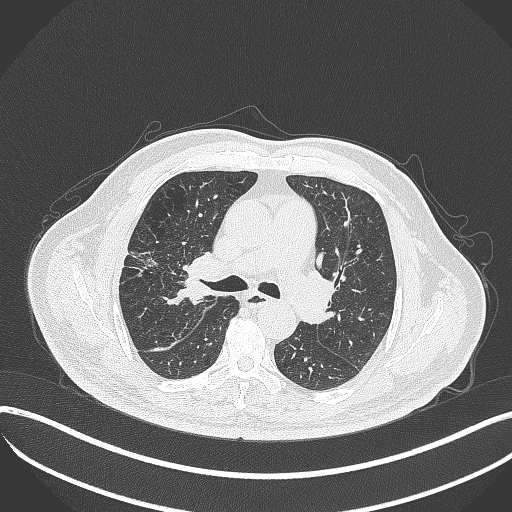
Chest CT, one axial slice; slice 224 of 401 in the series (ordered by position); reconstruction kernel B70f; 120 kVp; lung window (W 1500 / L -600 HU); 1 mm slice thickness; 512 × 512 image matrix, field of view 400 × 400 mm. Male patient, age 72 years. Case-level facts recorded for this patient, not image findings: clinical TNM (as recorded): T1c N0 M0; histopathological grade: G2.
Structures marked on this image (rectangle marked by the reading radiologist):
- lung tumour (recorded histology: squamous cell carcinoma): bounding box (x1, y1, x2, y2) in pixels: (165, 255, 204, 310)